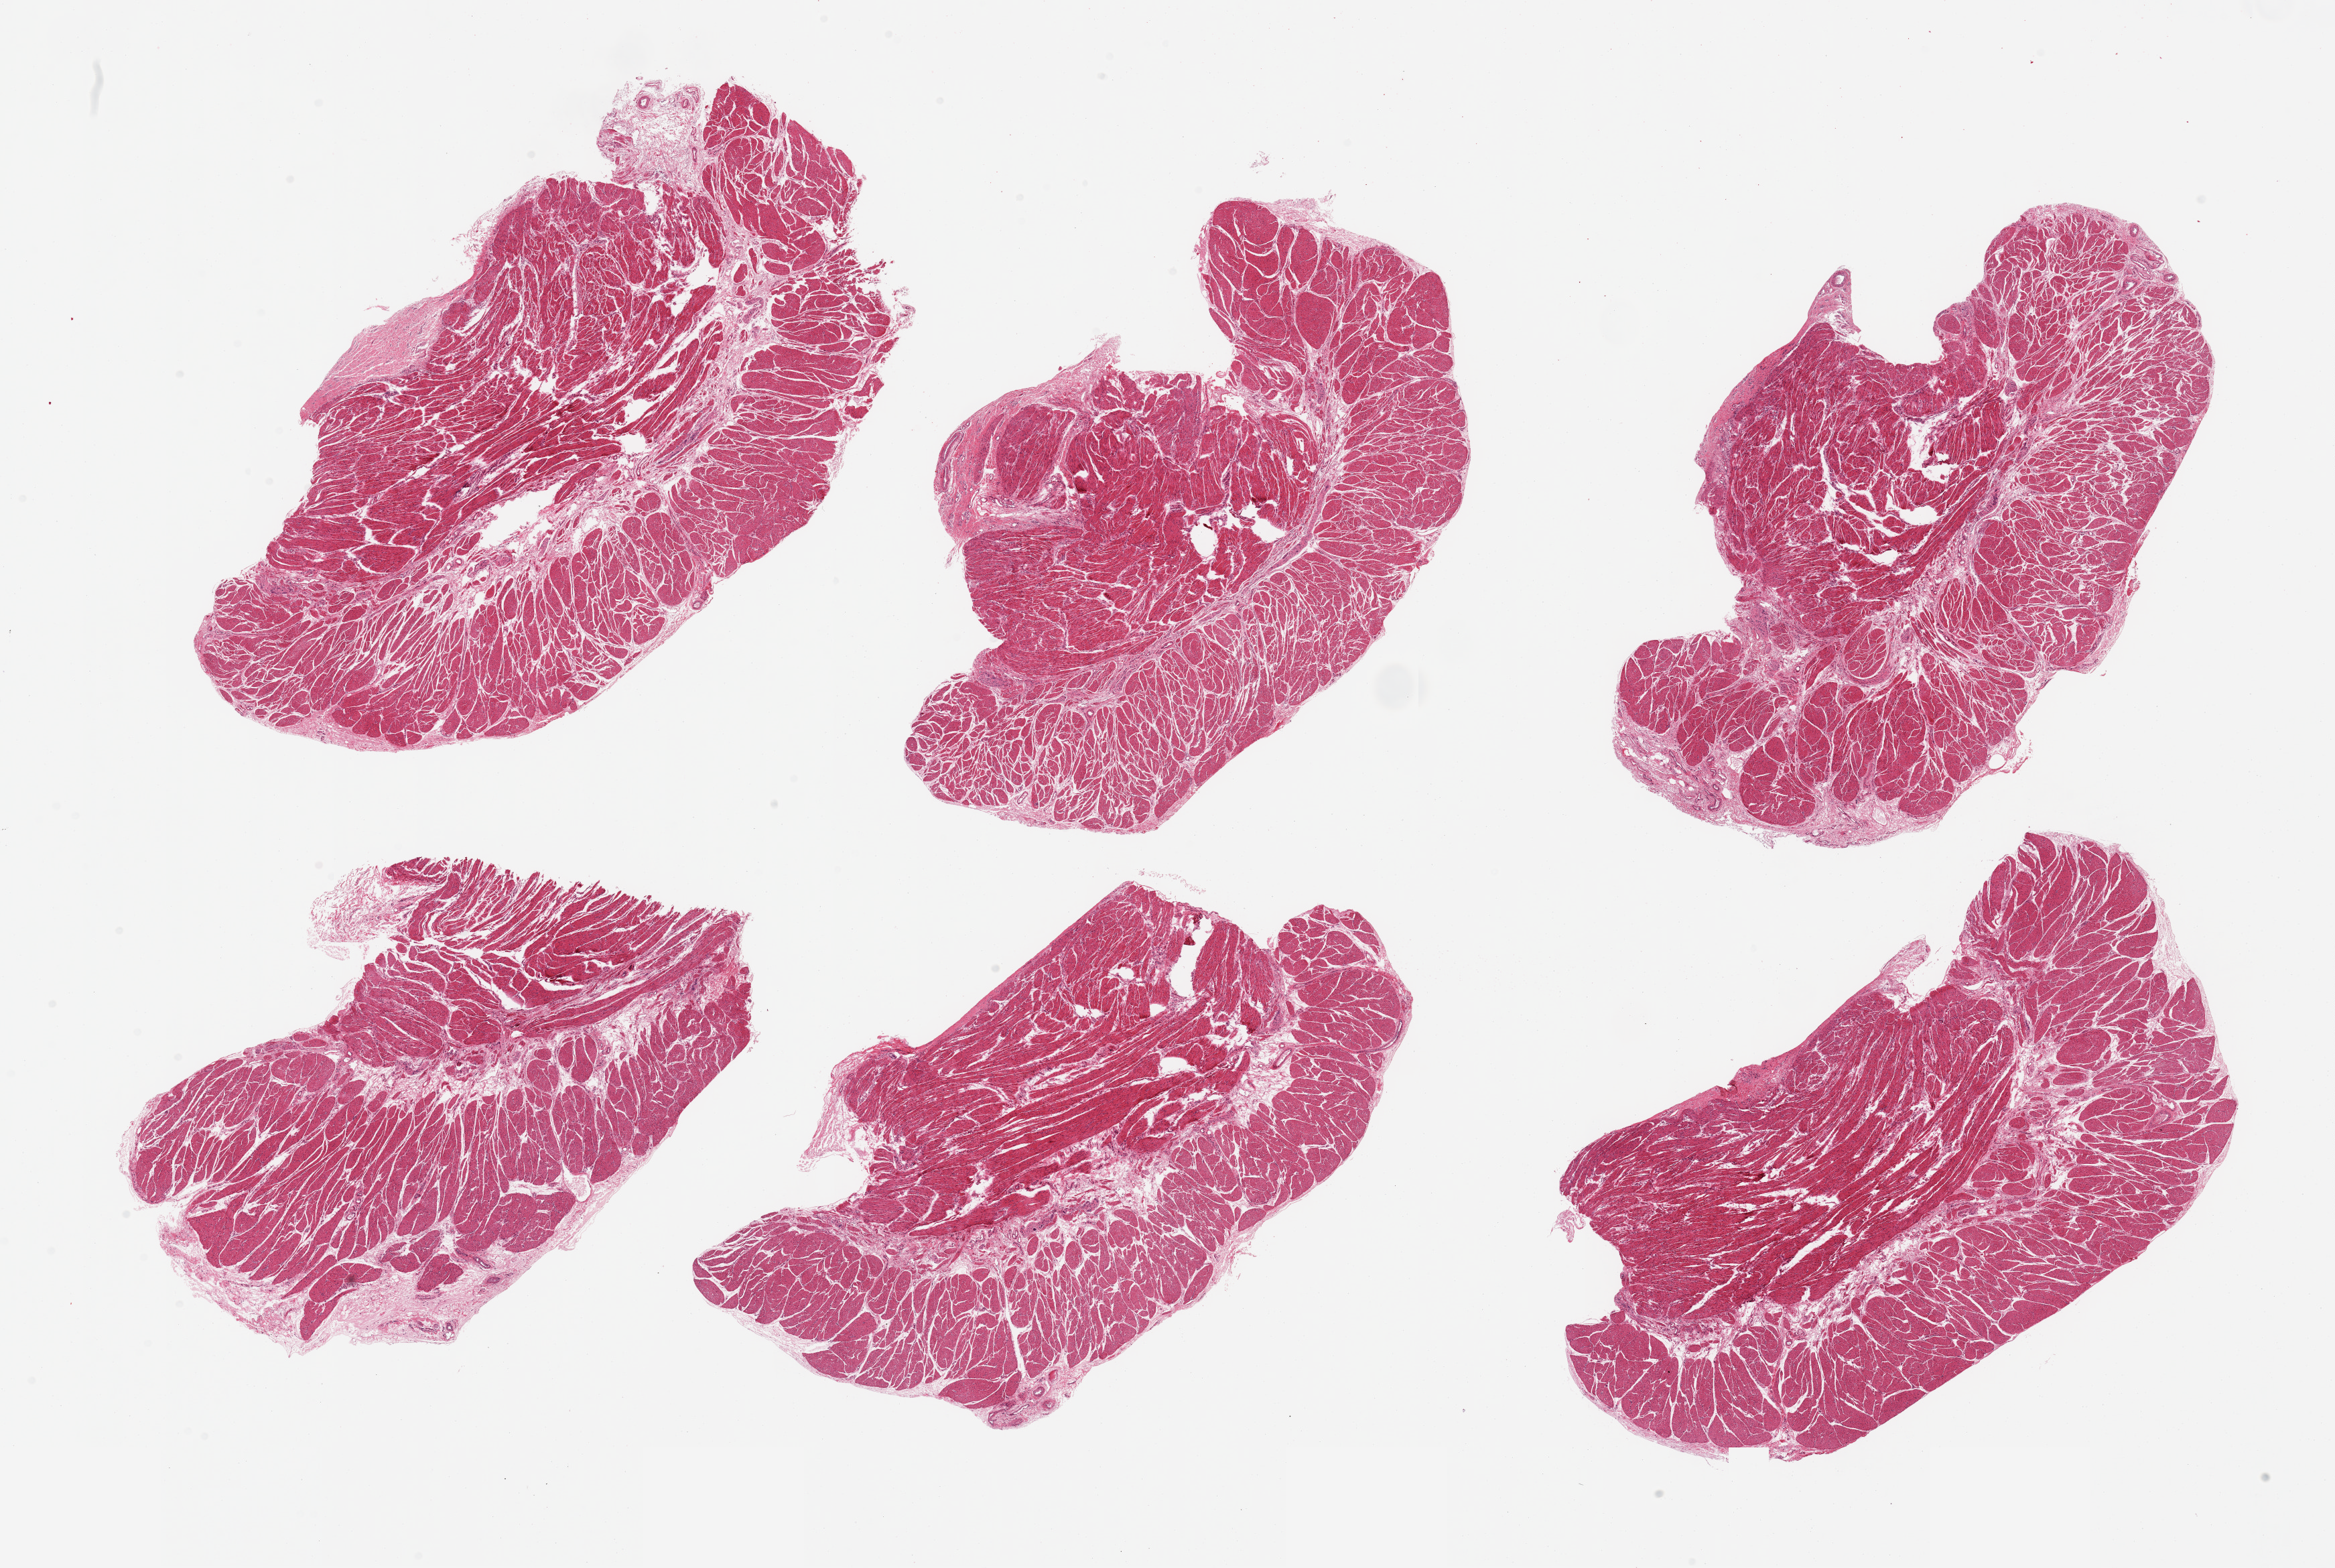
Digitized hematoxylin and eosin (H&E)-stained section, whole scanned area (about 27.6 x 18.5 mm) shown as a low-resolution overview, PAXgene-fixed paraffin-embedded (PFPE) section, sampled site (target tissue): gastroesophageal junction, donor tissue sample. Donor: female.
Pathologist's review note for this sample: 6 pieces, confirmed target muscularis.